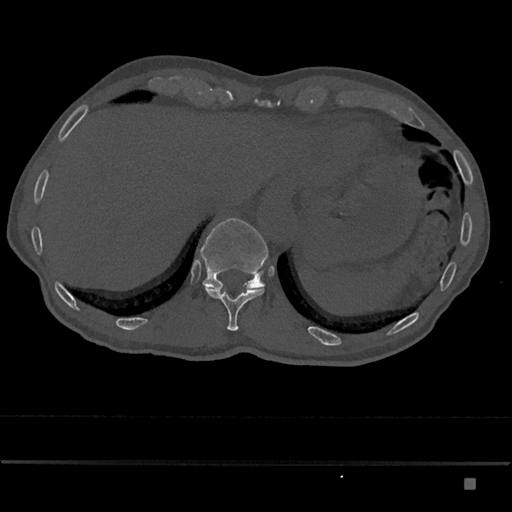
CT including the spine, one axial slice; slice 650 of 797 in the series (ordered by position); 120 kVp; bone window (W 1800 / L 400 HU); 0.5 mm slice thickness; 512 × 512 image matrix. Male patient, age 72 years. Case-level facts recorded for this patient, not image findings: primary cancer: prostate.
Annotated regions visible in this slice (semi-automatic segmentation, software-assisted and operator-edited):
- T11 vertebra: bounding box <203,284,265,331> (left, top, right, bottom; pixels)
- T12 vertebra: <200,218,268,289>